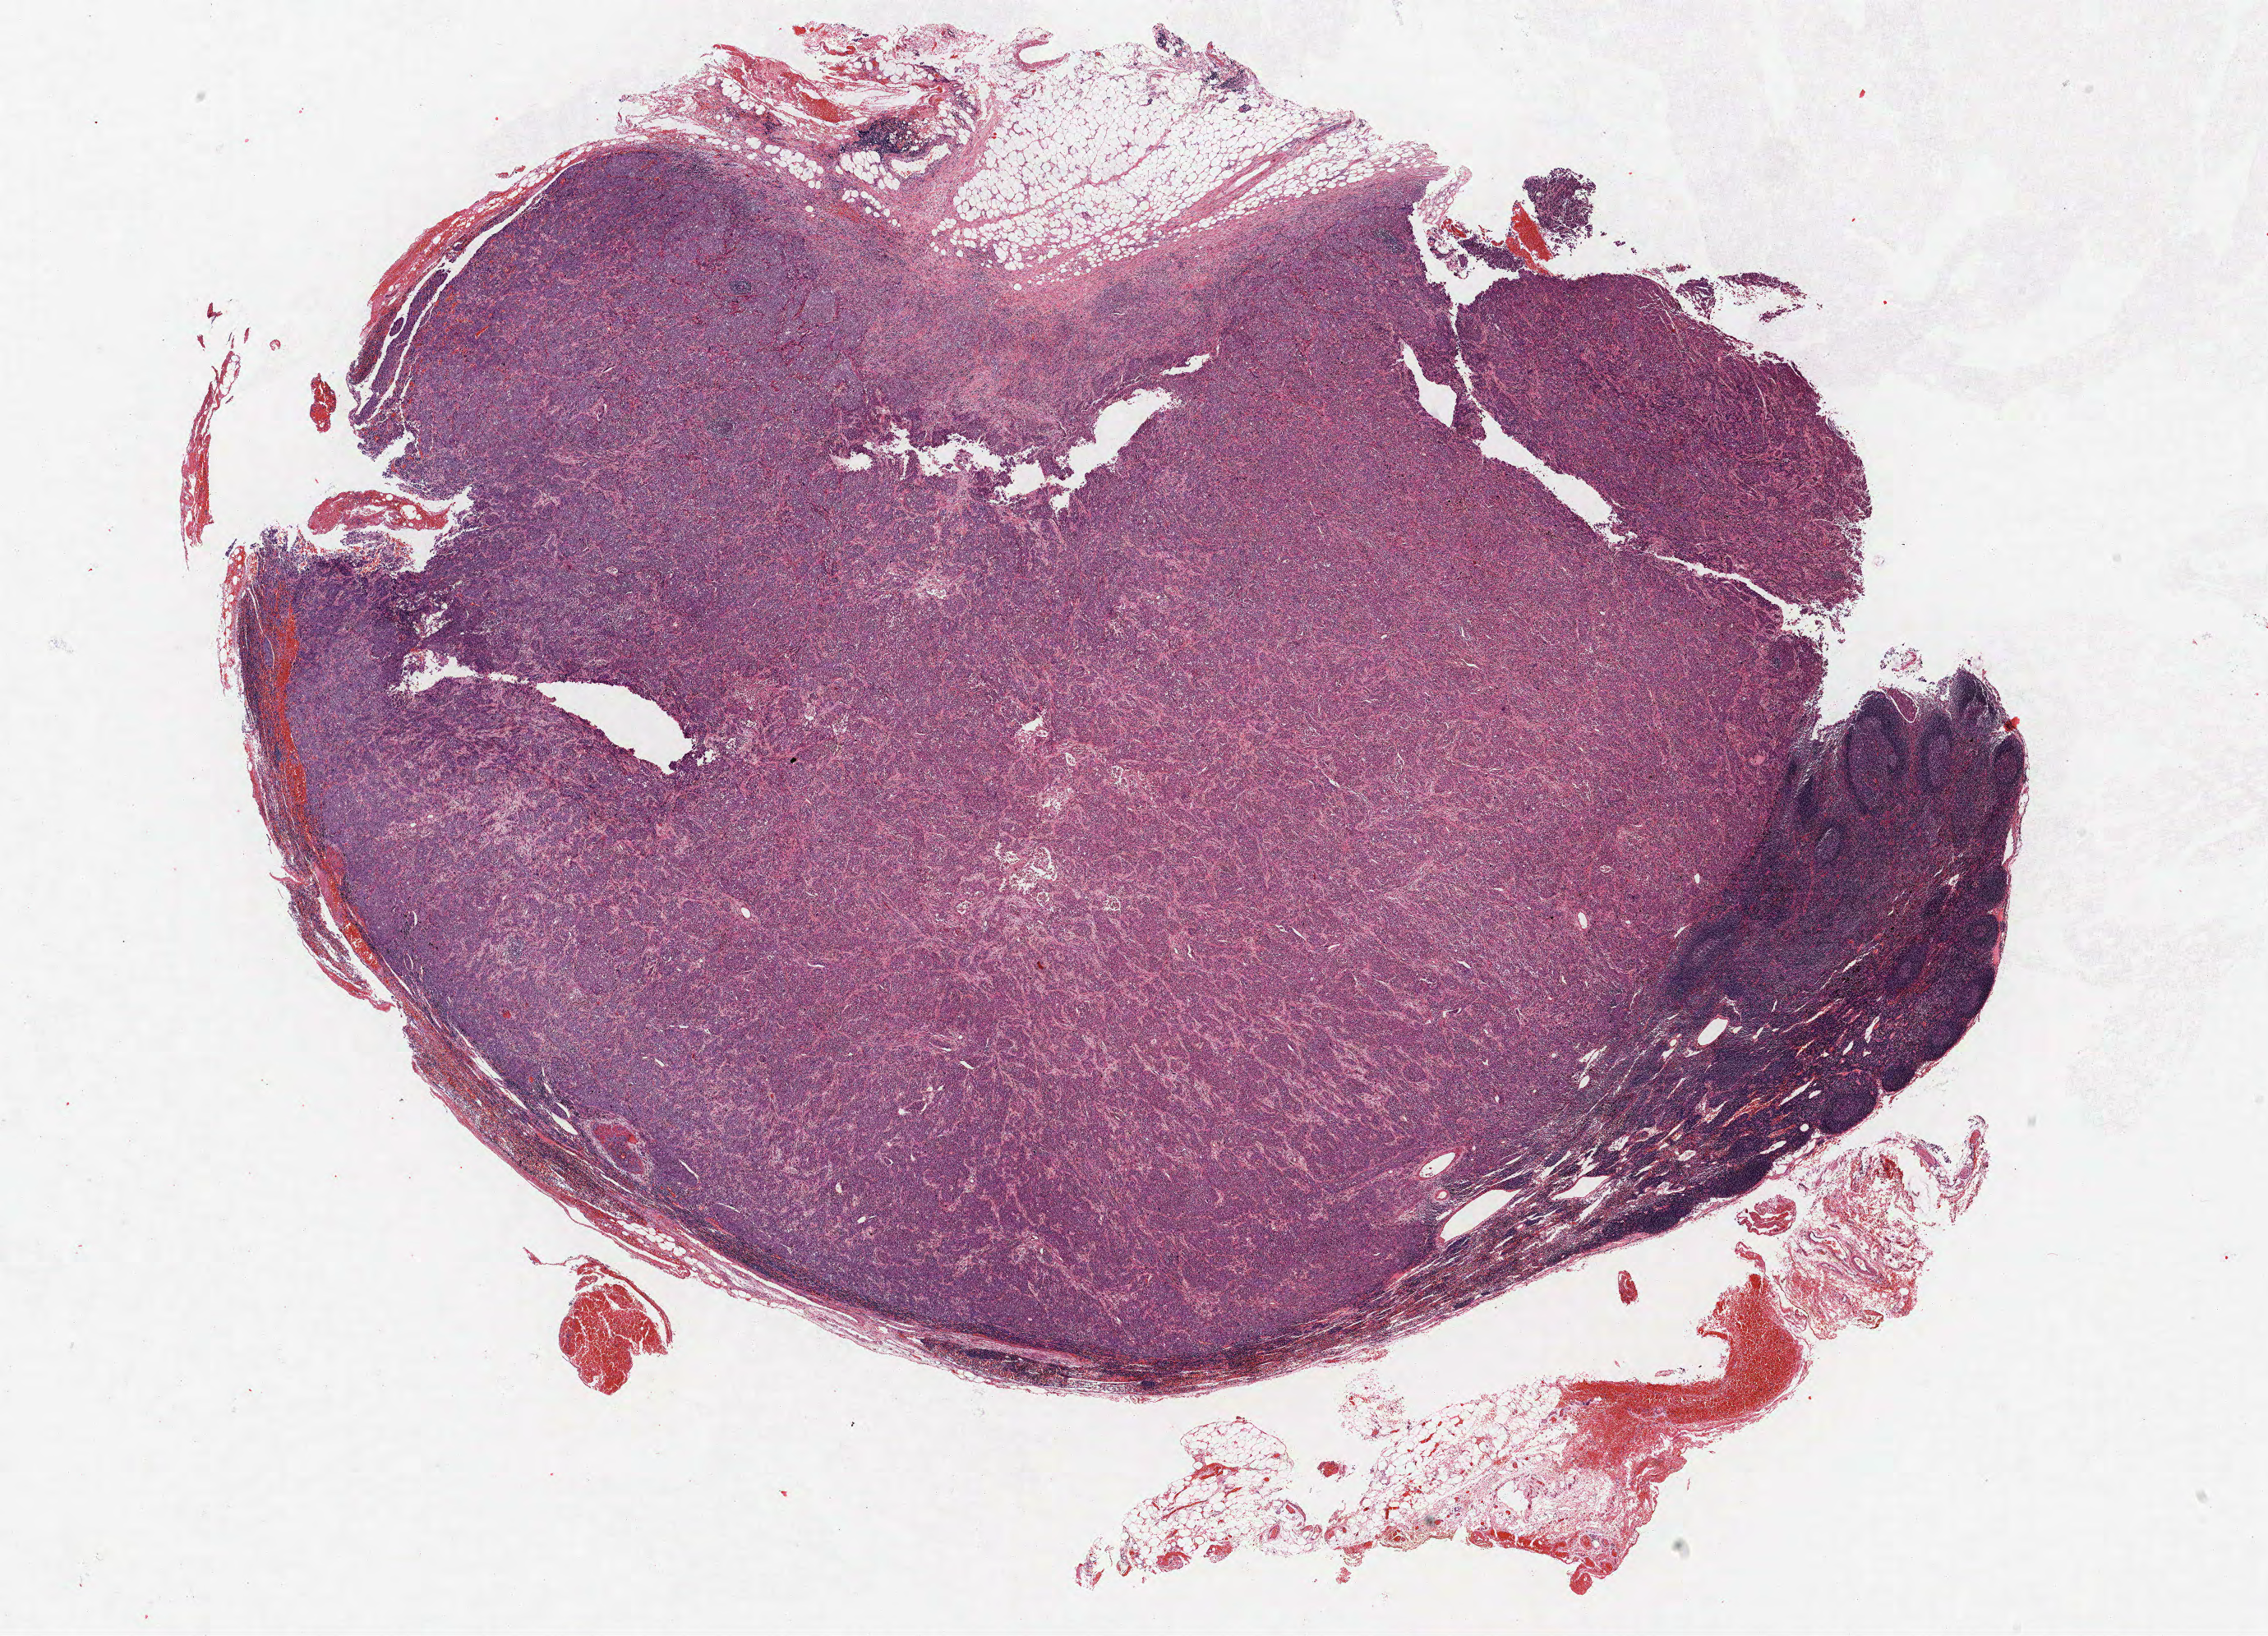
Whole-slide histology image, Hematoxylin and eosin (H&E) stained, shown as a low-resolution overview of the whole scanned area (about 22.1 x 15.9 mm, acquisition: 40x scan), formalin-fixed paraffin-embedded (FFPE) section, lung. Male, age 60 at enrolment. Former smoker at enrolment. Grade: poorly differentiated (G3).
Tumour size (pathology): 35 mm. Primary tumour location (clinical record): right lower lobe. Participant's lung-cancer diagnosis: Adenocarcinoma, NOS. Stage (AJCC 6th edition): IIB.